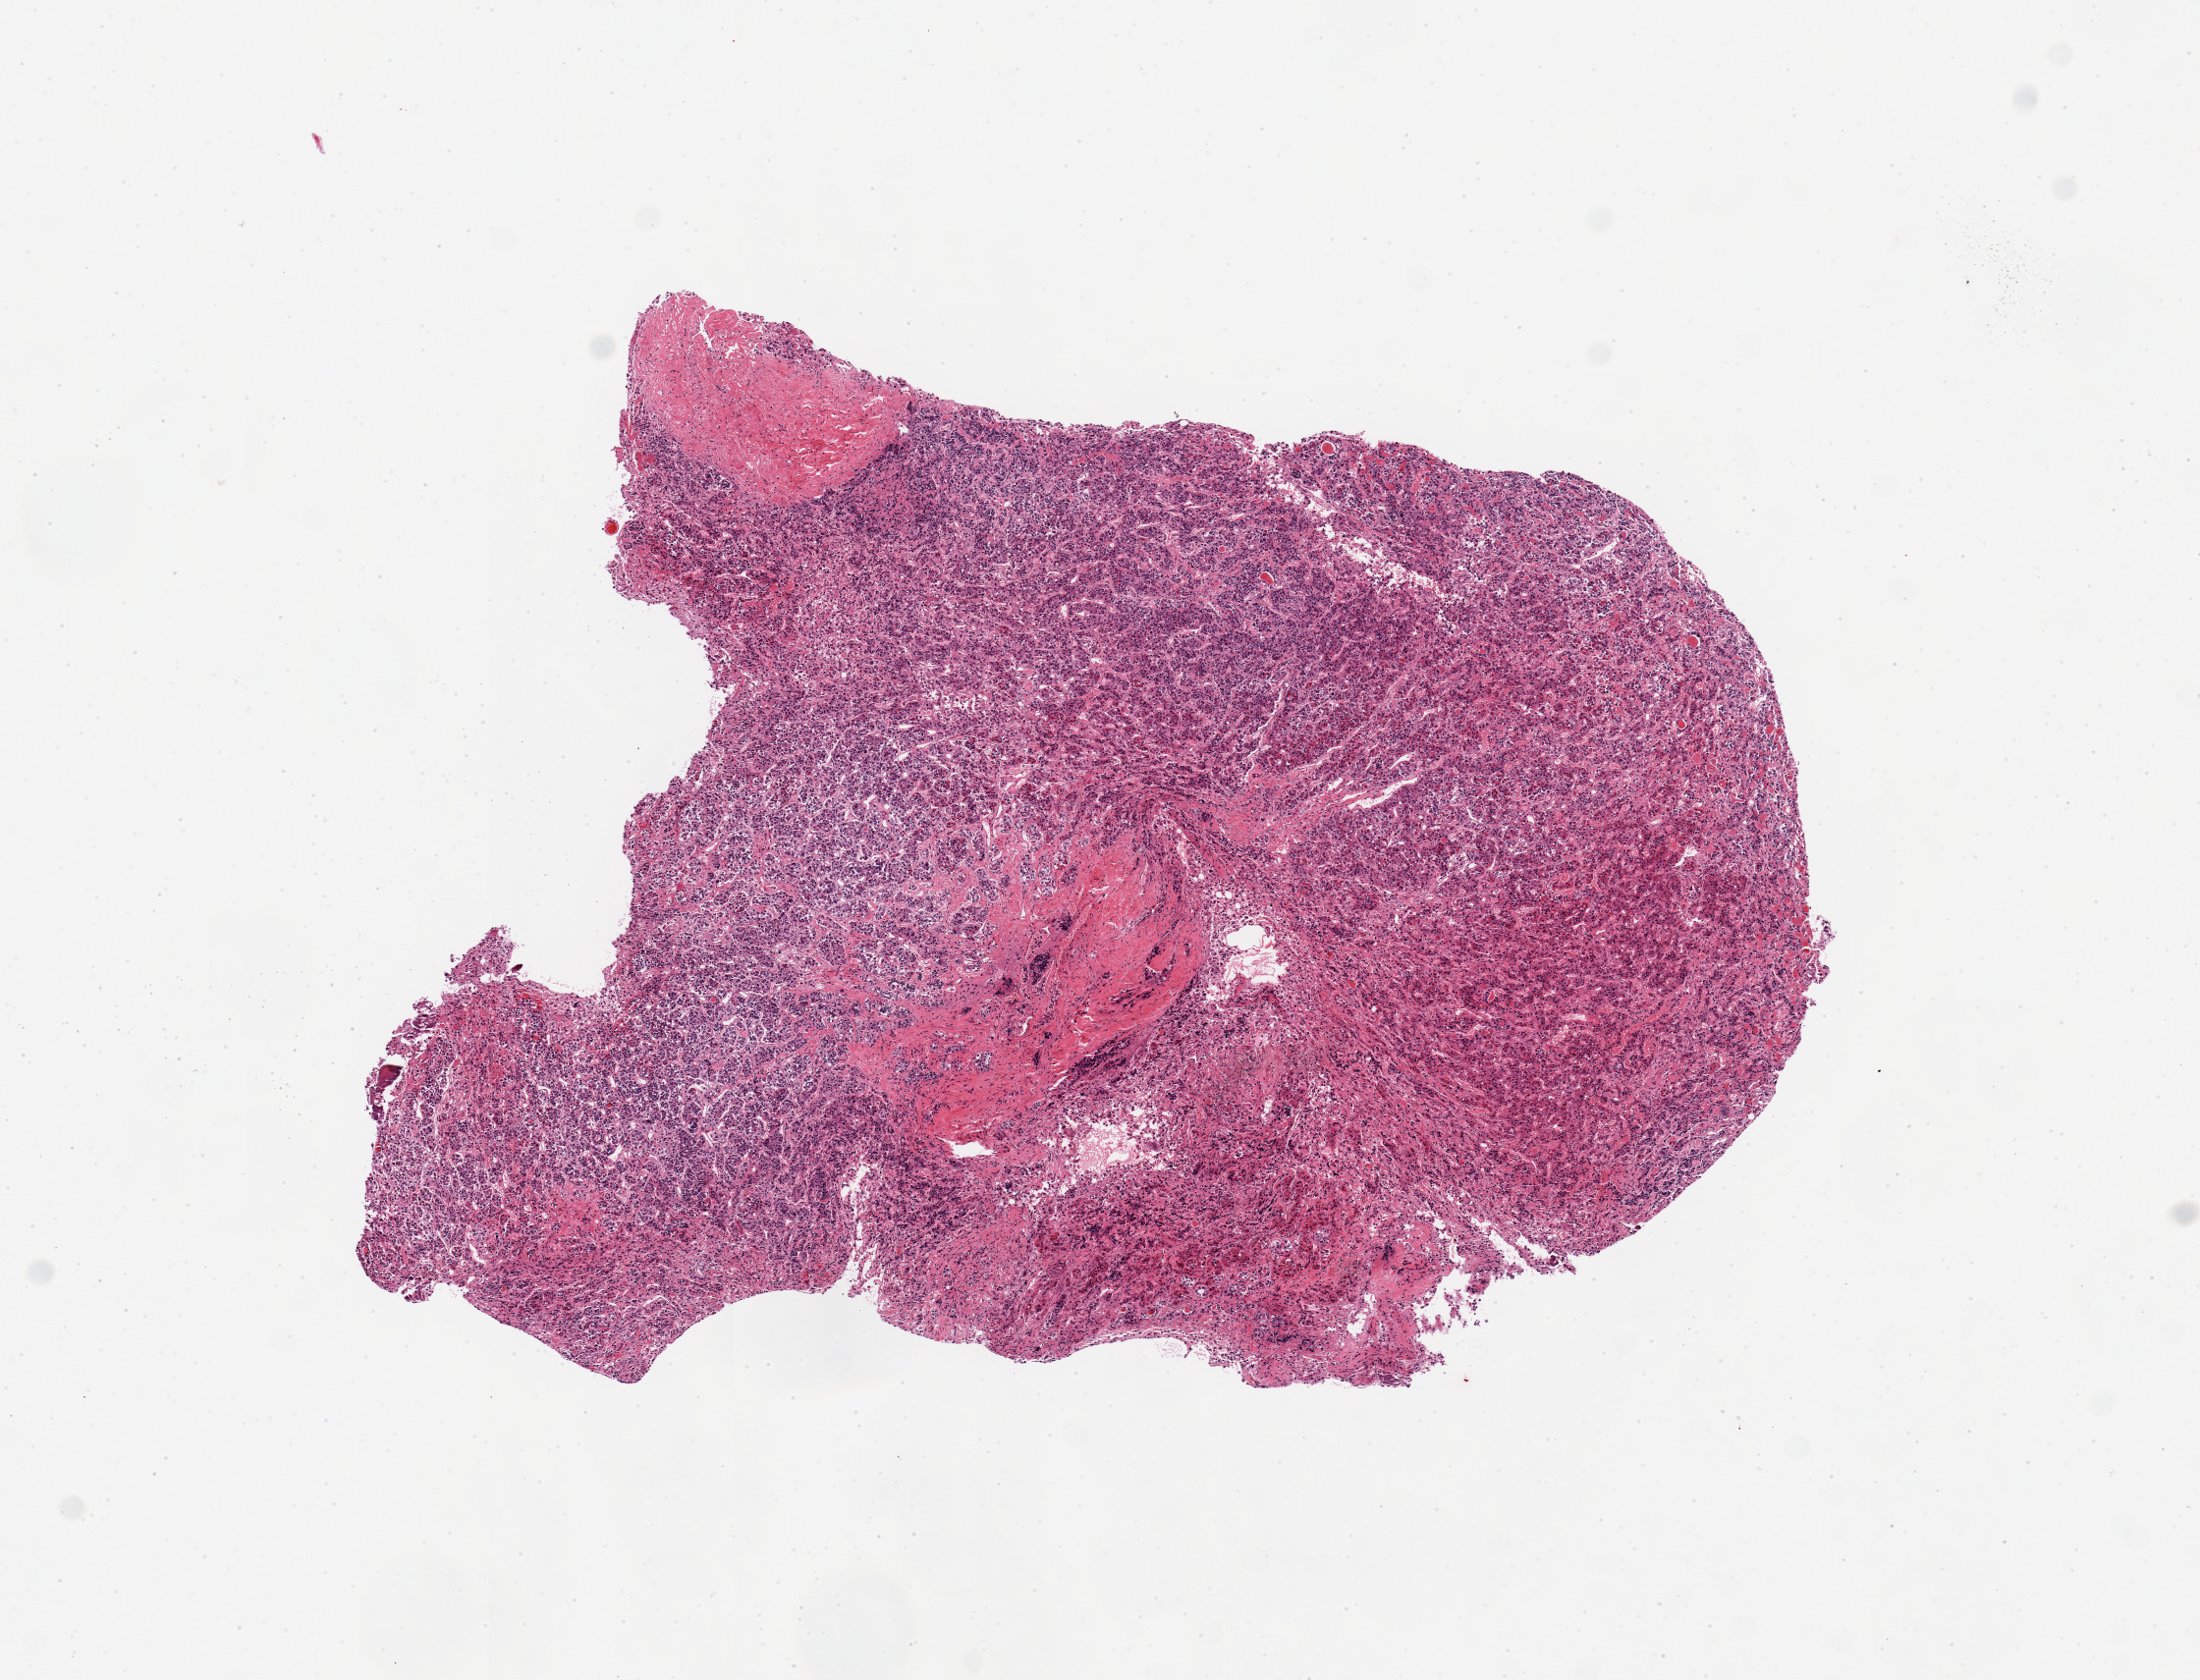
Haematoxylin and eosin whole-slide image, brightfield — low-resolution overview of the scanned area, about 8.9 x 6.8 mm (slide scanned at 20x). PAXgene-fixed paraffin-embedded (PFPE) section. Sampled site (target tissue): pituitary. Tissue donor sample. Donor sex: male.
- reviewer comment on this tissue sample: 1 piece, all adenohypophysis, 1x0.5mm nubbin of dura